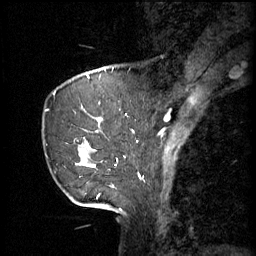
Breast MRI (dynamic contrast-enhanced), one sagittal slice; slice 14 of 60 in the series (ordered by position); 3 images stored at this slice position (order not interpretable as contrast timing); 1.5 T; TE 4.2 ms, TR 11 ms; 256 × 256 image matrix, field of view 220 × 220 mm. Patient: female, 69 years.
Structures marked on this image (semi-automatic segmentation, software-assisted and operator-edited):
- analysis volume of interest (the breast-tissue region the enhancement analysis was run in; not a lesion): bounding box (x1, y1, x2, y2) in pixels: (45, 88, 116, 189)
- tumour enhancement mask (voxels above the 70 % enhancement threshold inside the analysis volume of interest): (83, 162, 93, 167)